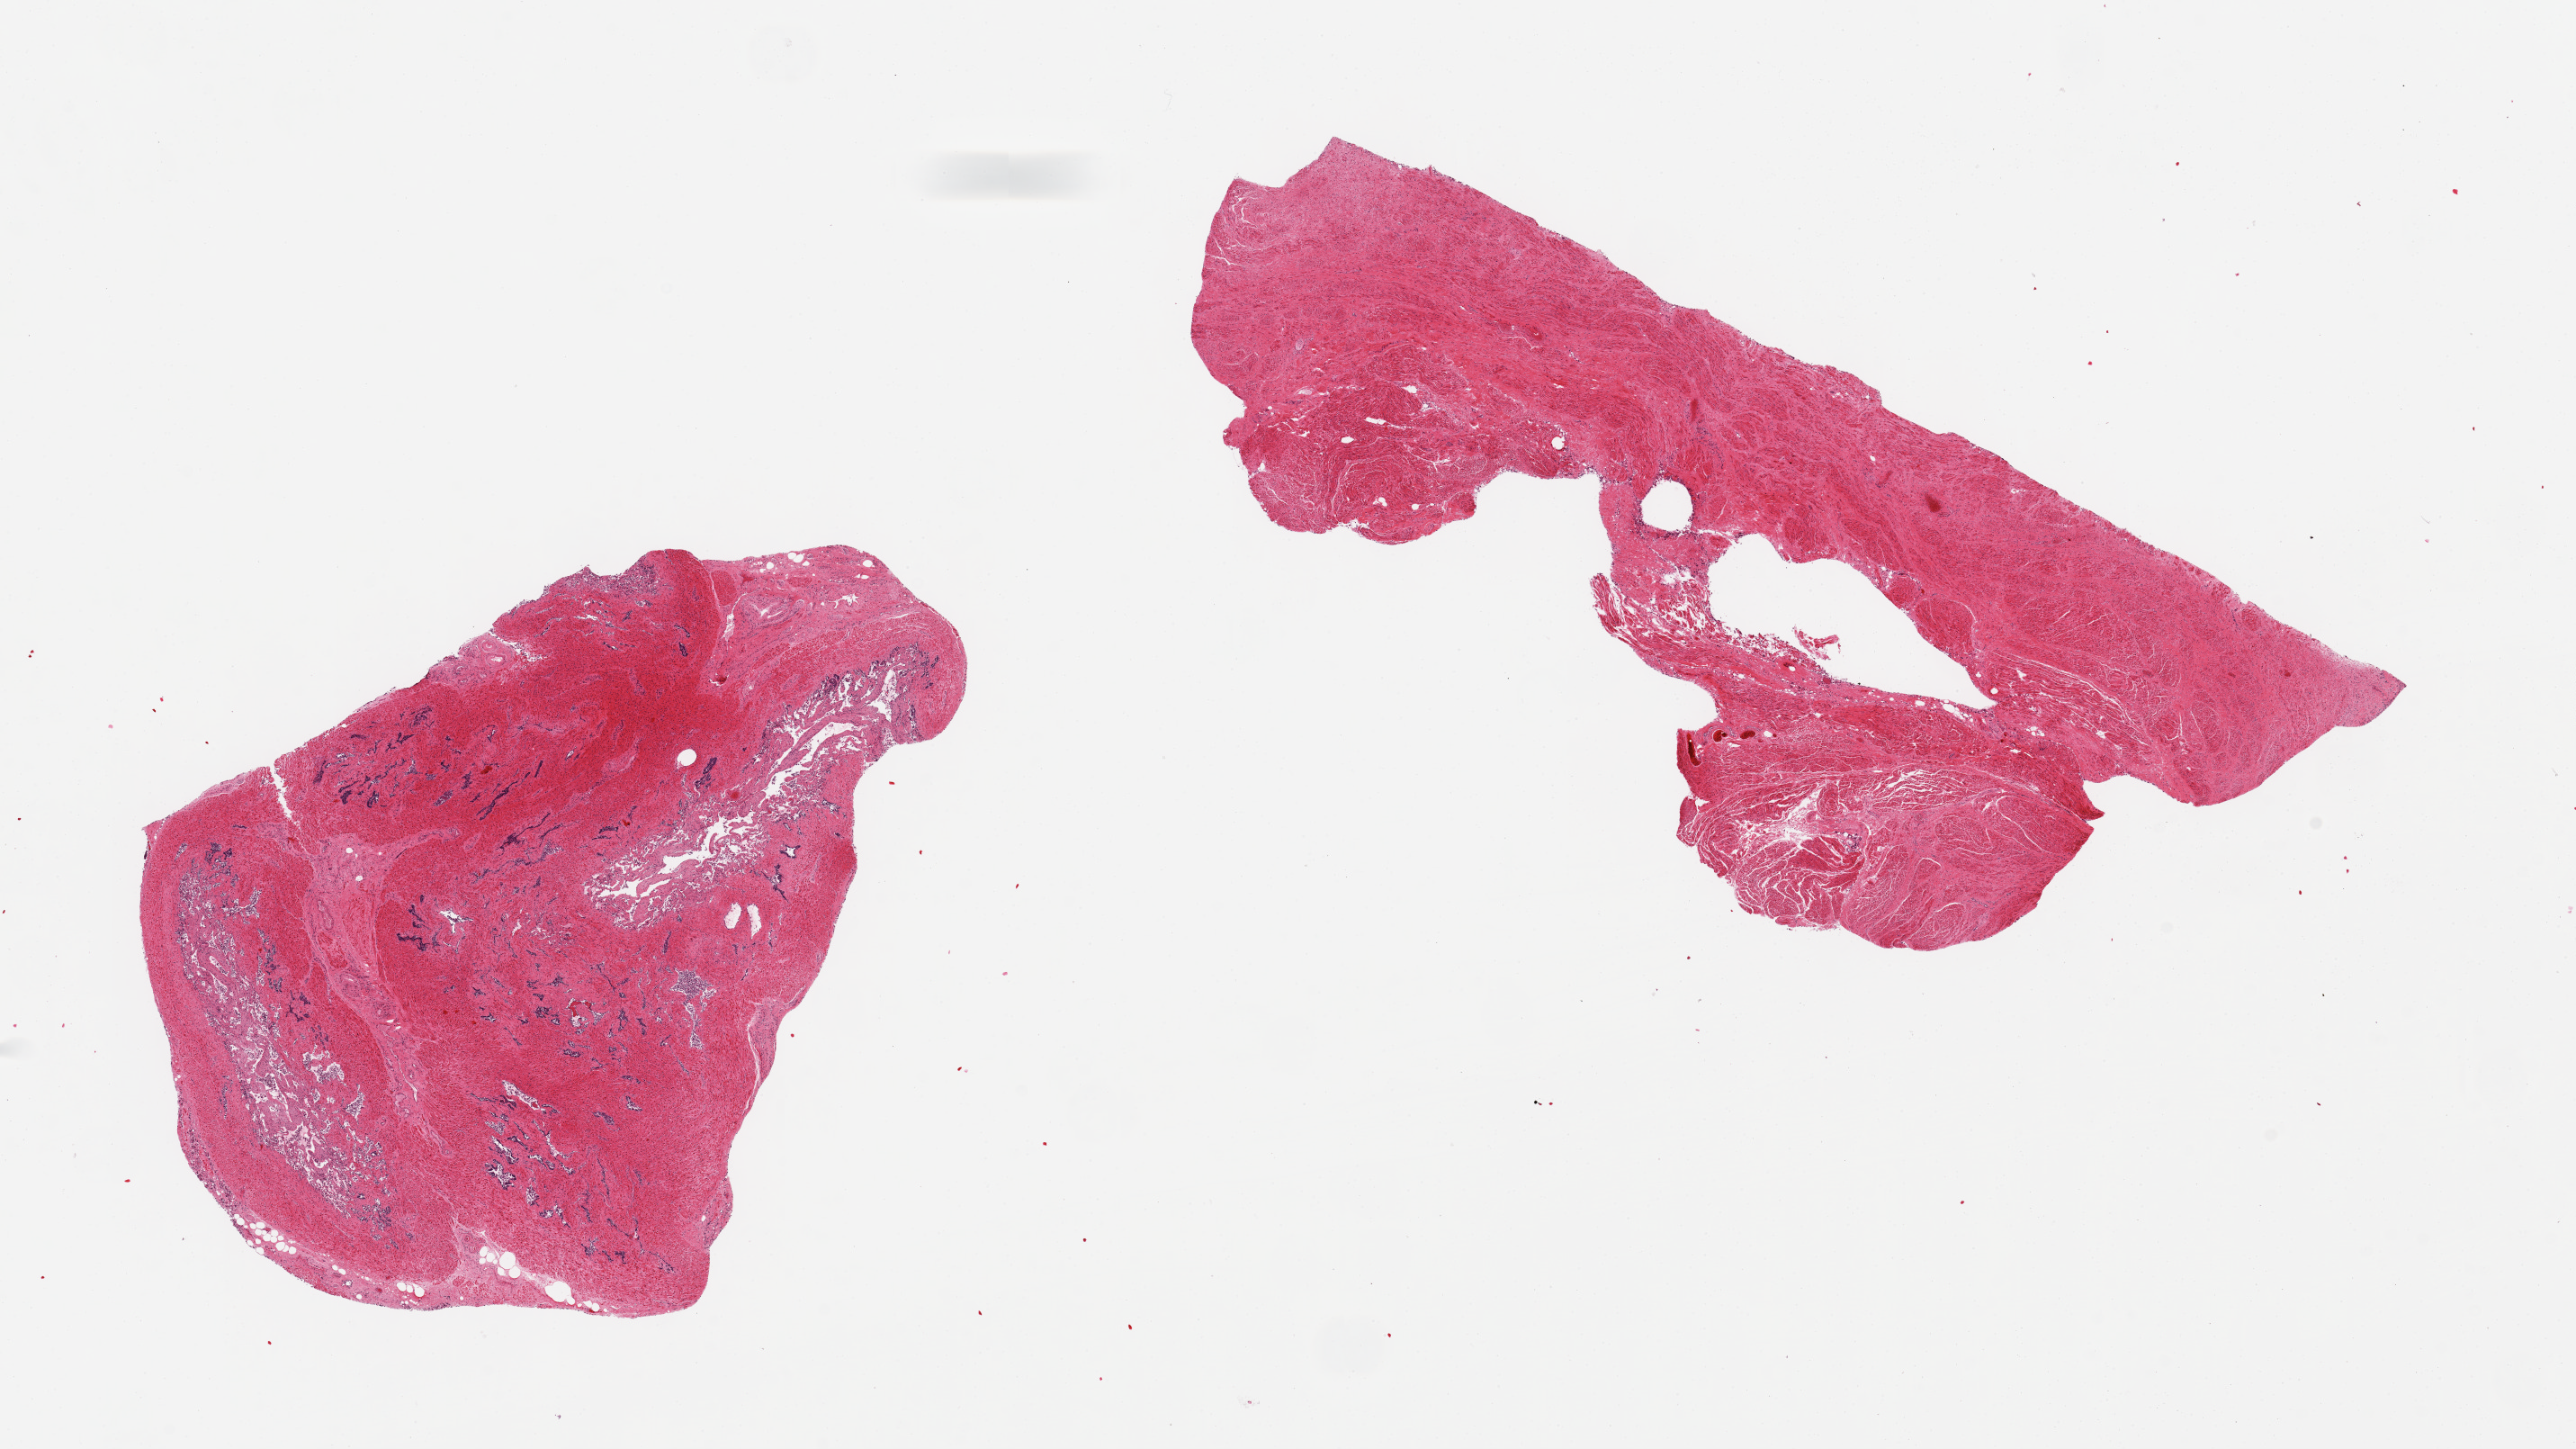
Digitized haematoxylin and eosin-stained section — low-resolution overview of the scanned area, about 22.6 x 12.7 mm. PAXgene-fixed paraffin-embedded (PFPE) section. Section of prostate (target tissue). Tissue donor sample. Donor sex: male.
- review note (as recorded): 2 pieces, glandular component in one section badly autolyzed; may be partially seminal vesicle